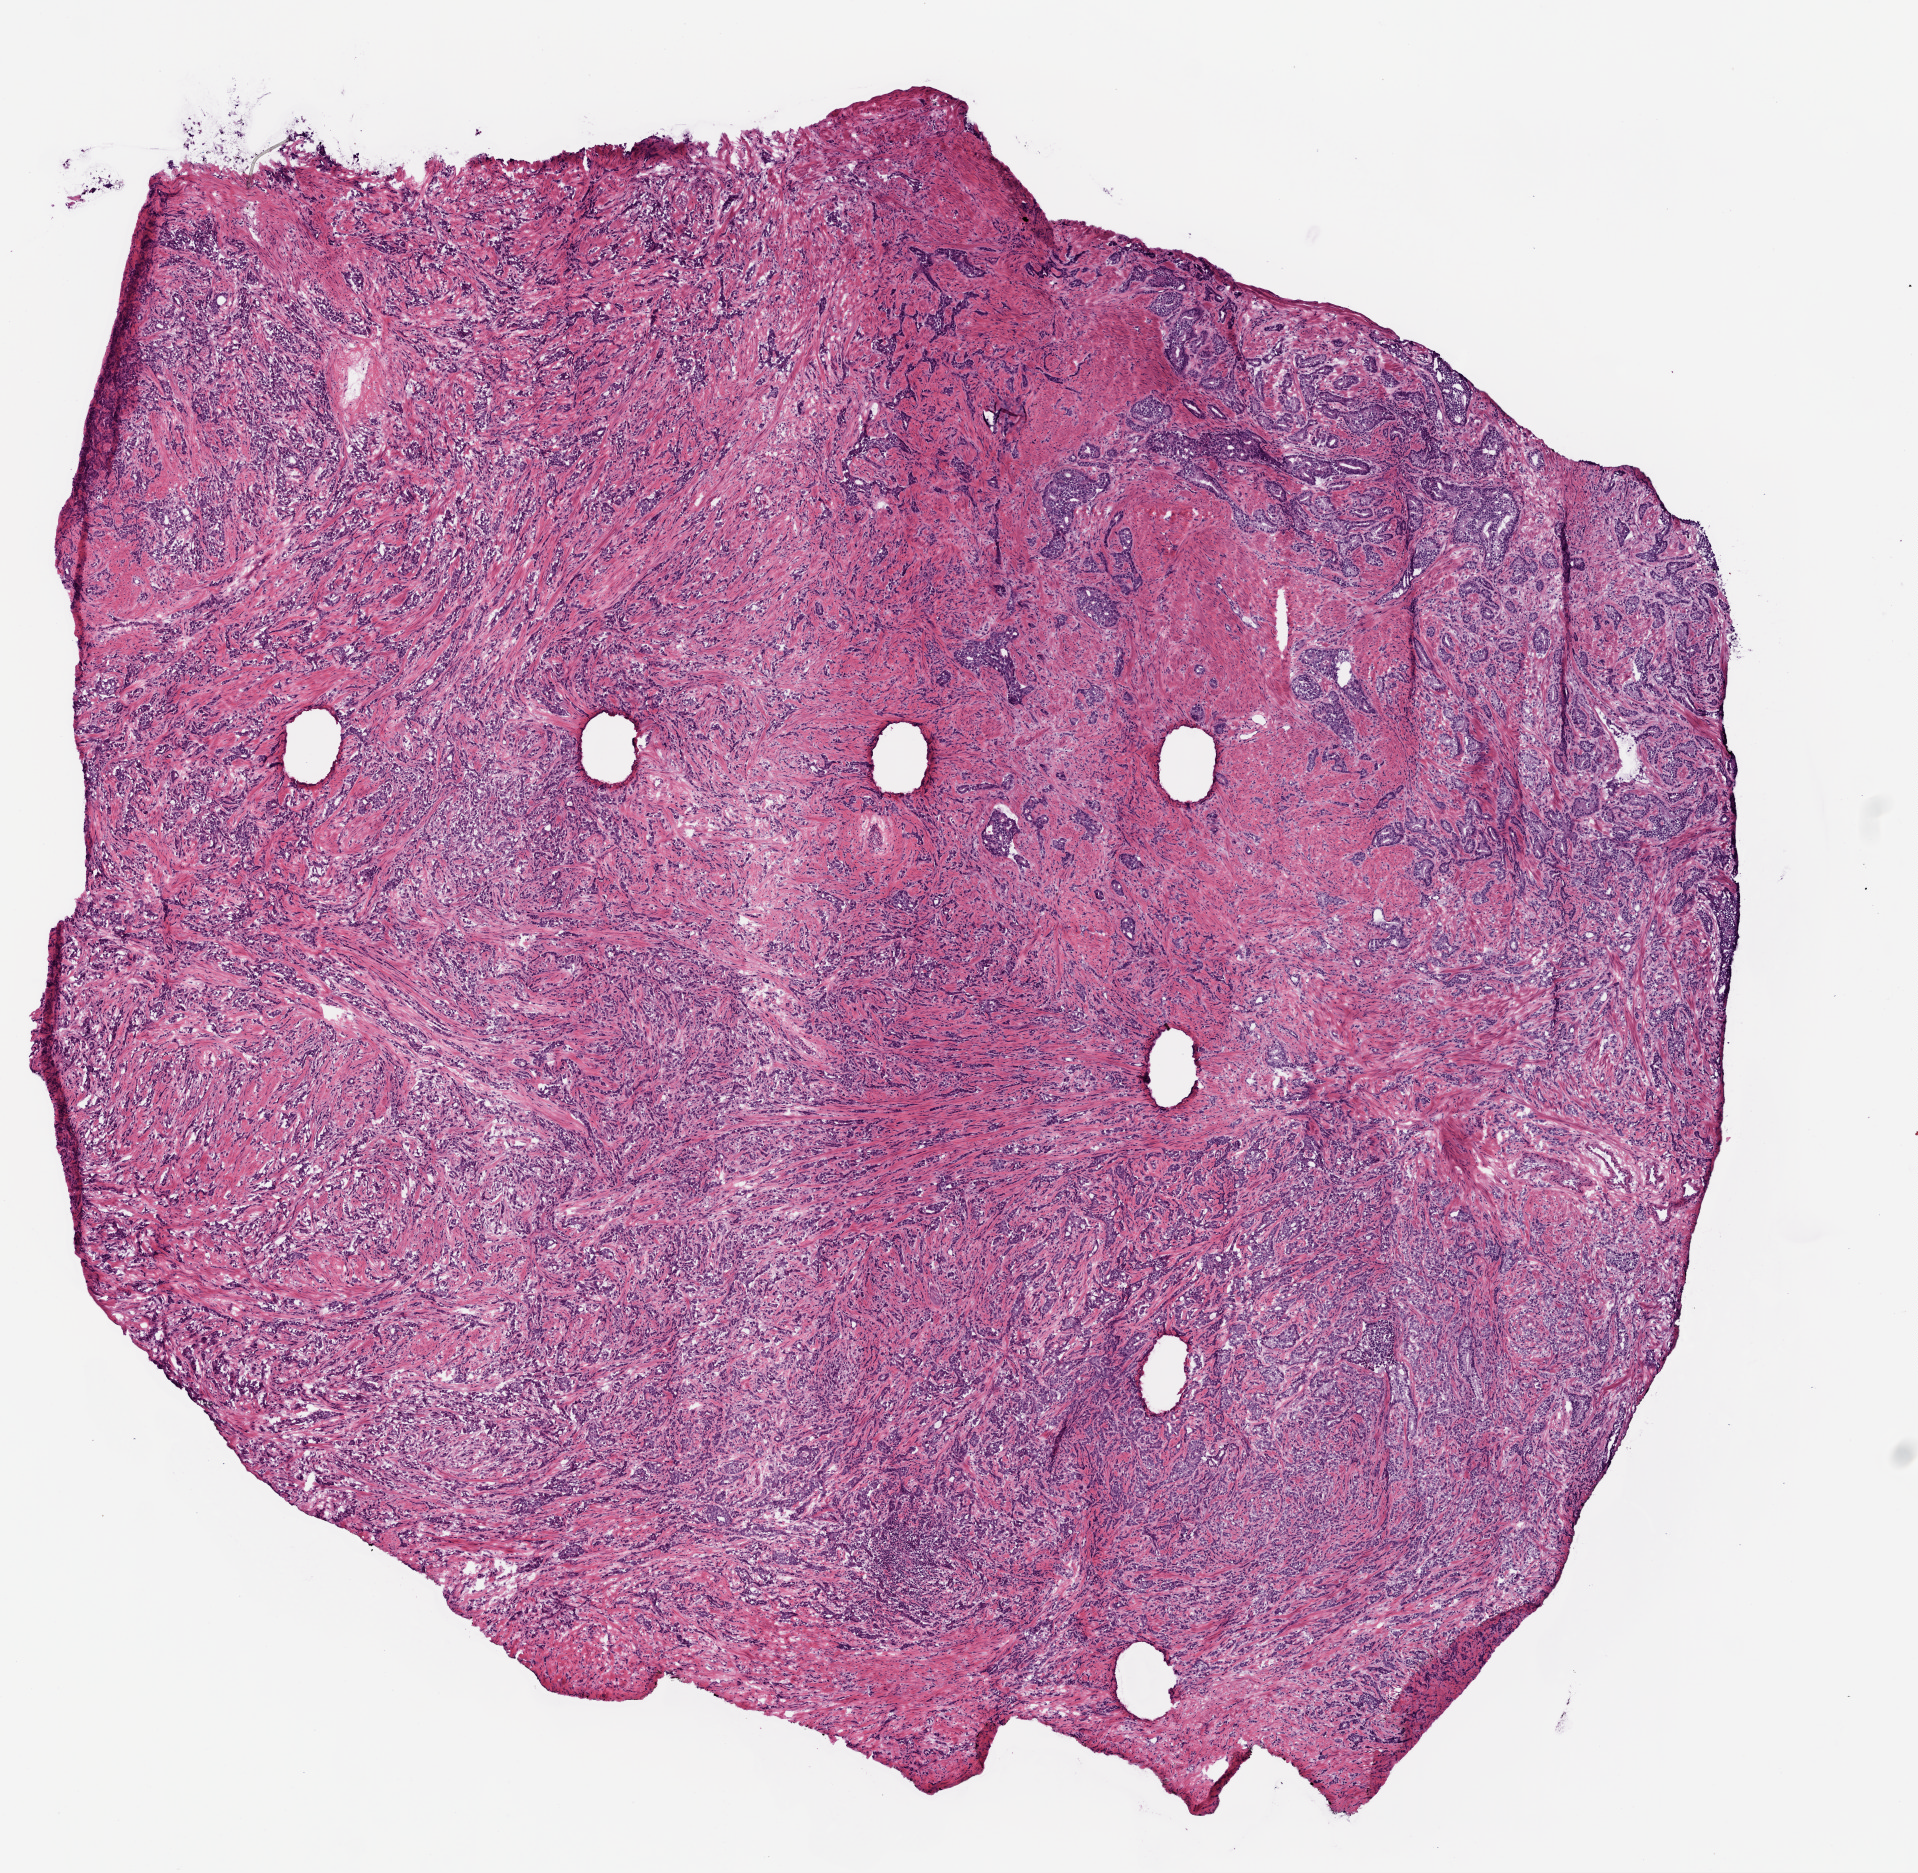
H&E-stained whole-slide image, a low-resolution overview of the entire scanned area, about 7.7 x 7.6 mm (from a 20x scan). Frozen section. Sample: primary tumour, prostate. Male, age 54 years at initial diagnosis. Gleason score: 8 (4+4). Pathologist review of this section (percent, as recorded): tumour nuclei 65%, necrosis 0%.
* histologic diagnosis: Acinar cell carcinoma (prostate gland)